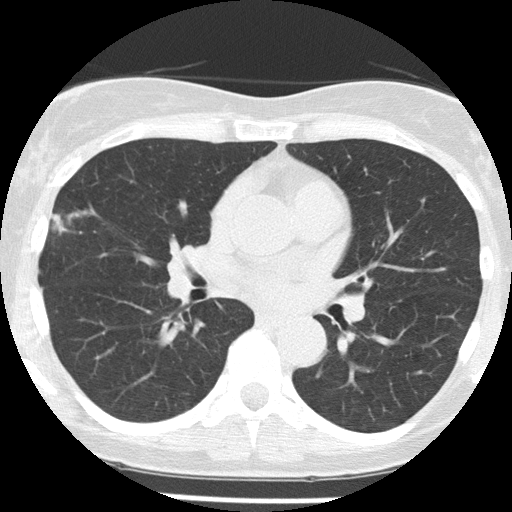
Axial slice from a low-dose chest CT screening exam; baseline screening round; lung window (W 1500 / L -600 HU); slice 71 of 156 in the series. Female, age 58 years at enrolment. Former smoker at enrolment.
Lesion marked by an expert reader, bounding box (x1, y1, x2, y2) in pixels: (27, 195, 90, 257). The exam's reader record, not a measurement of the box and not confirmed to be the same lesion: non-calcified nodule or mass ≥4 mm, right middle lobe, 18 × 9 mm, spiculated (stellate) margins, soft tissue attenuation. Later outcome: lung cancer diagnosed 79 days after this screen — non-small cell carcinoma, right middle lobe, poorly differentiated (G3), stage IA (AJCC 6th edition), 18 mm at pathology.